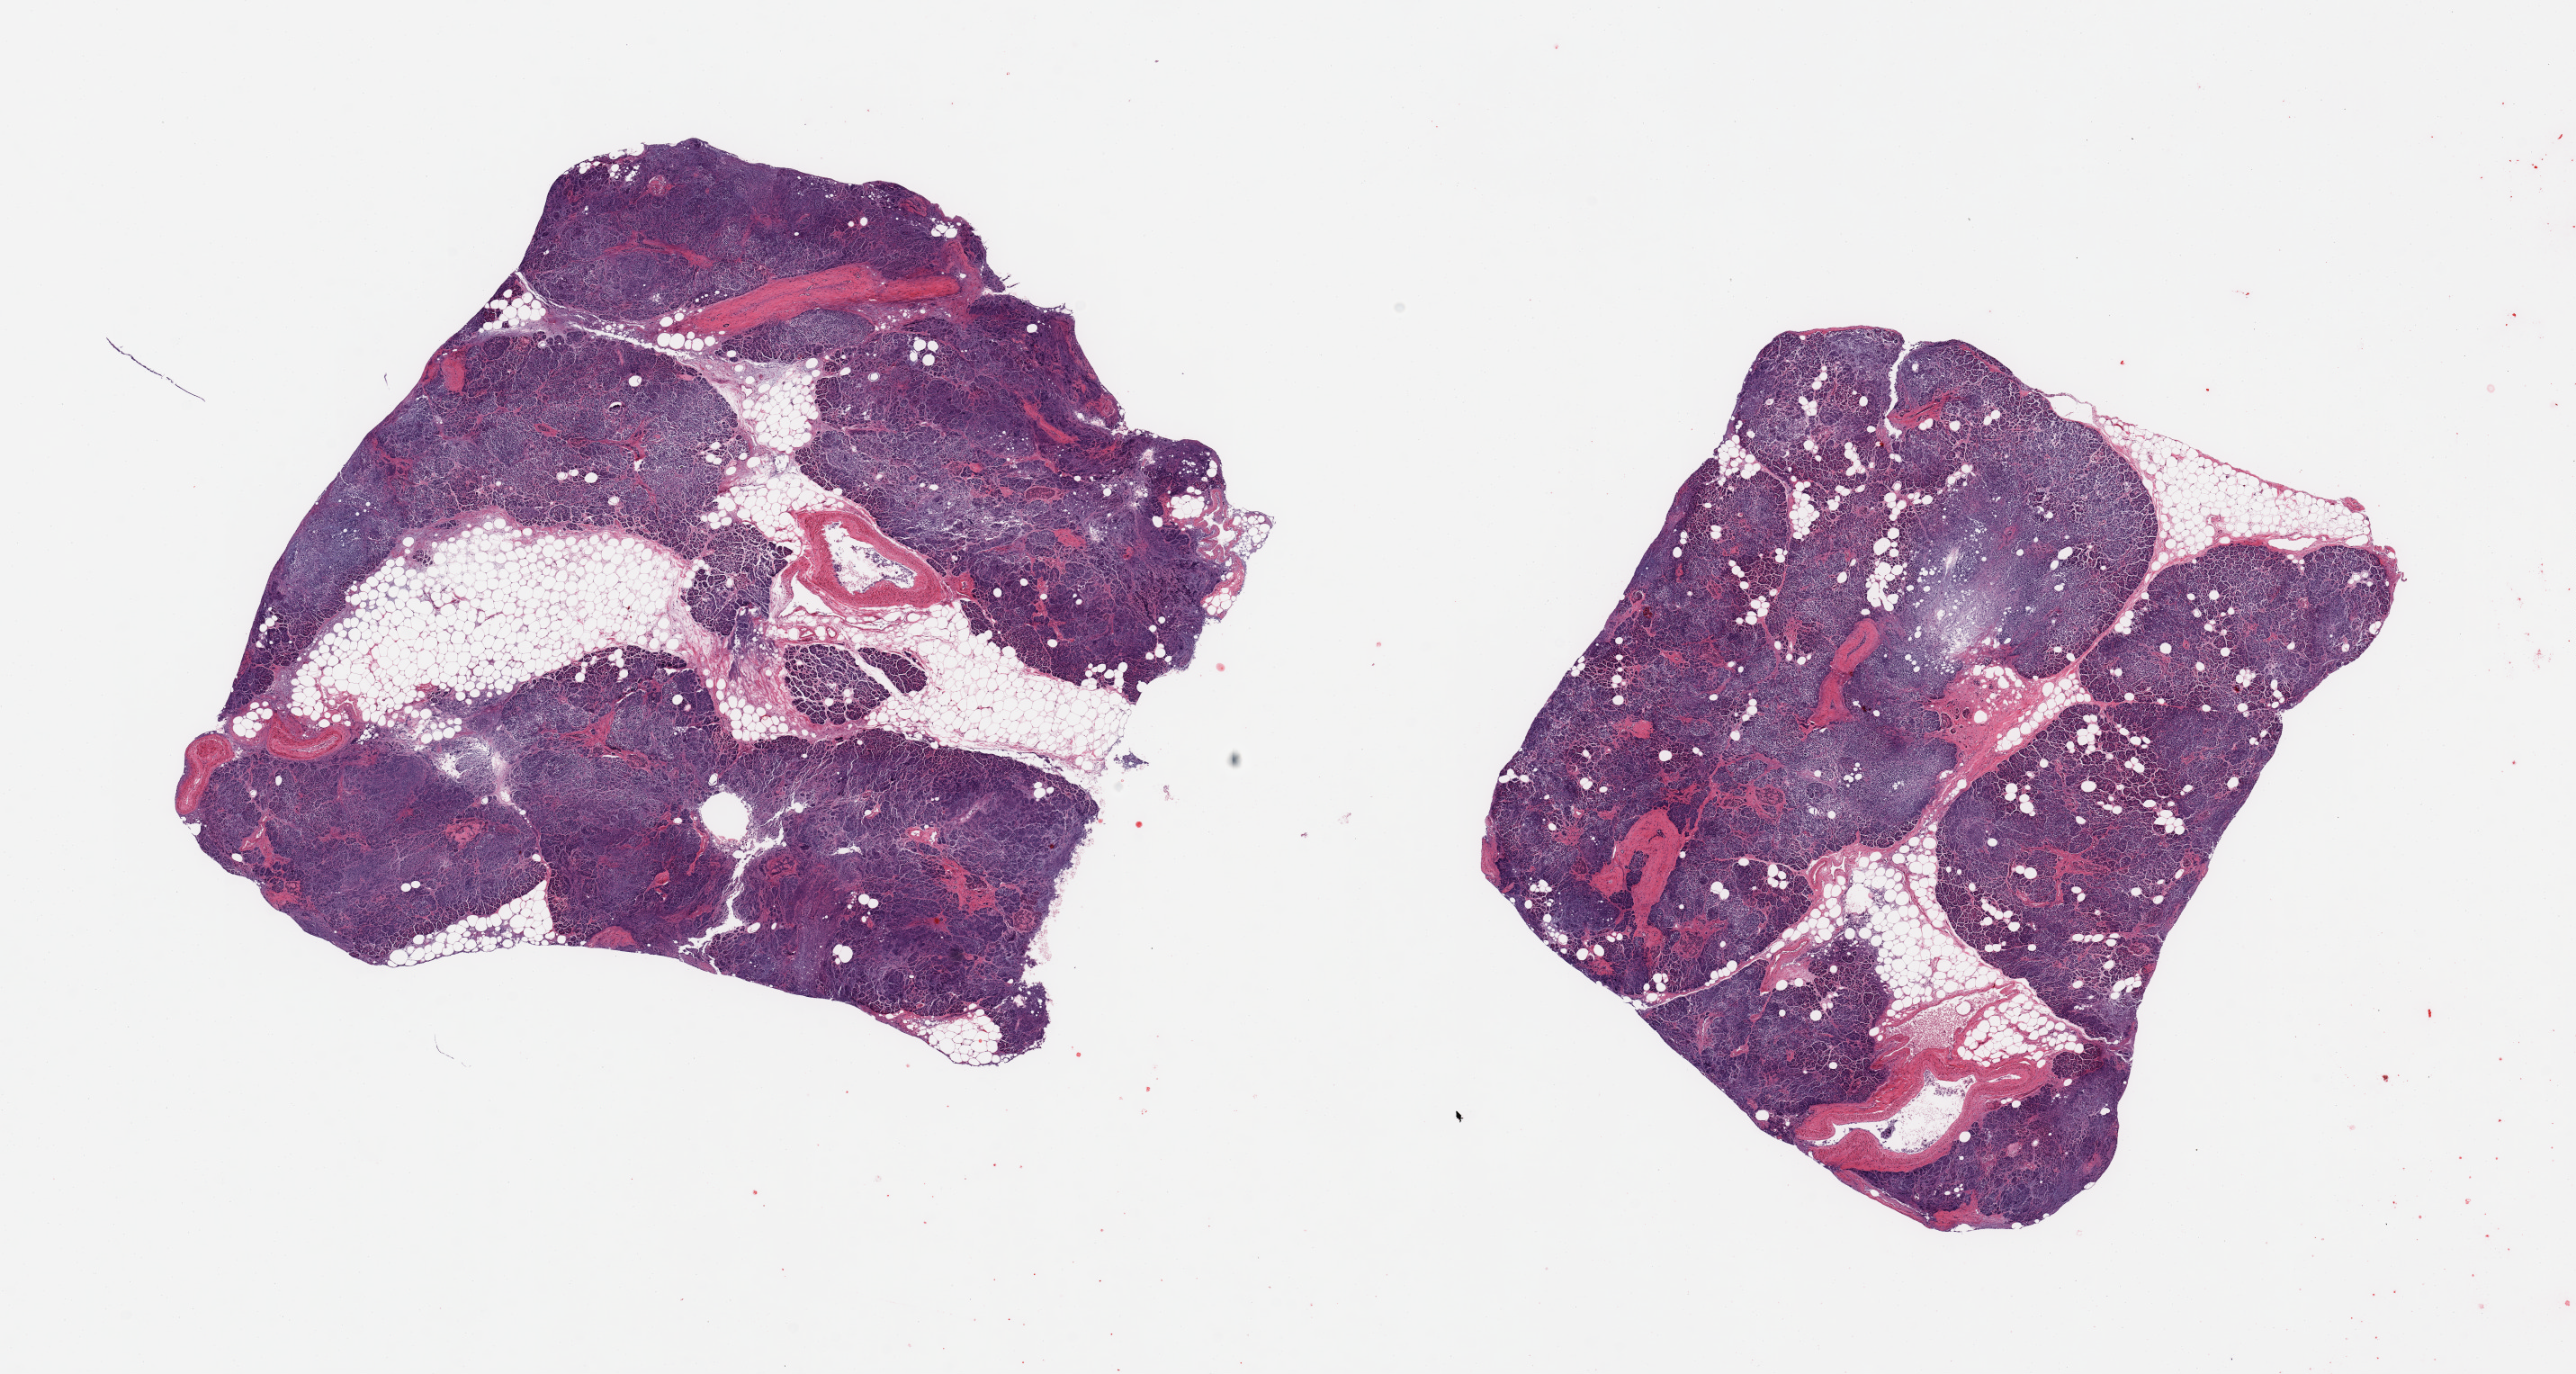
Haematoxylin and eosin whole-slide image, a low-resolution overview of the entire scanned area, about 22.6 x 12.1 mm. PAXgene-fixed, paraffin-embedded tissue. Target tissue: pancreas. Tissue donor sample. Male donor.
Reviewer comment on this tissue sample: 2 pieces; autolysis varies from 2 to 3; 20 & 30% internal fat.